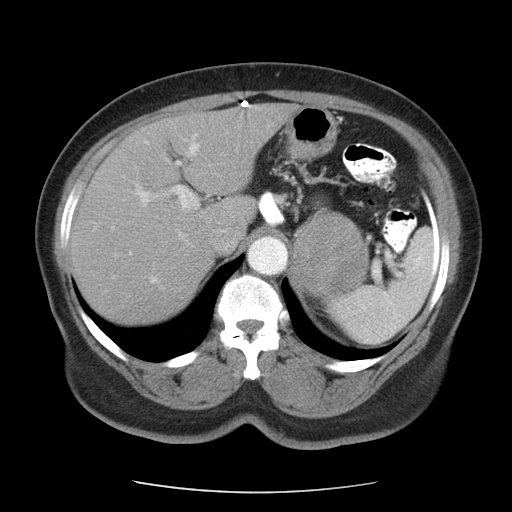
Contrast-enhanced abdominal CT, one axial slice. Slice 72 of 95 in the series (ordered by position). 120 kVp. Soft-tissue window (W 400 / L 40 HU). 512 × 512 image matrix. Female patient, age 71 years. From the clinical record (not read from this slice): diagnosis: adrenocortical carcinoma; tumour side: left adrenal; tumour size at pathology: 8.8 cm; Ki-67 index: 20 %; stage (as recorded): 2.
Annotated regions visible in this slice (semi-automatically segmented with operator editing):
- mass: box from (x=294, y=212) to (x=367, y=298) px